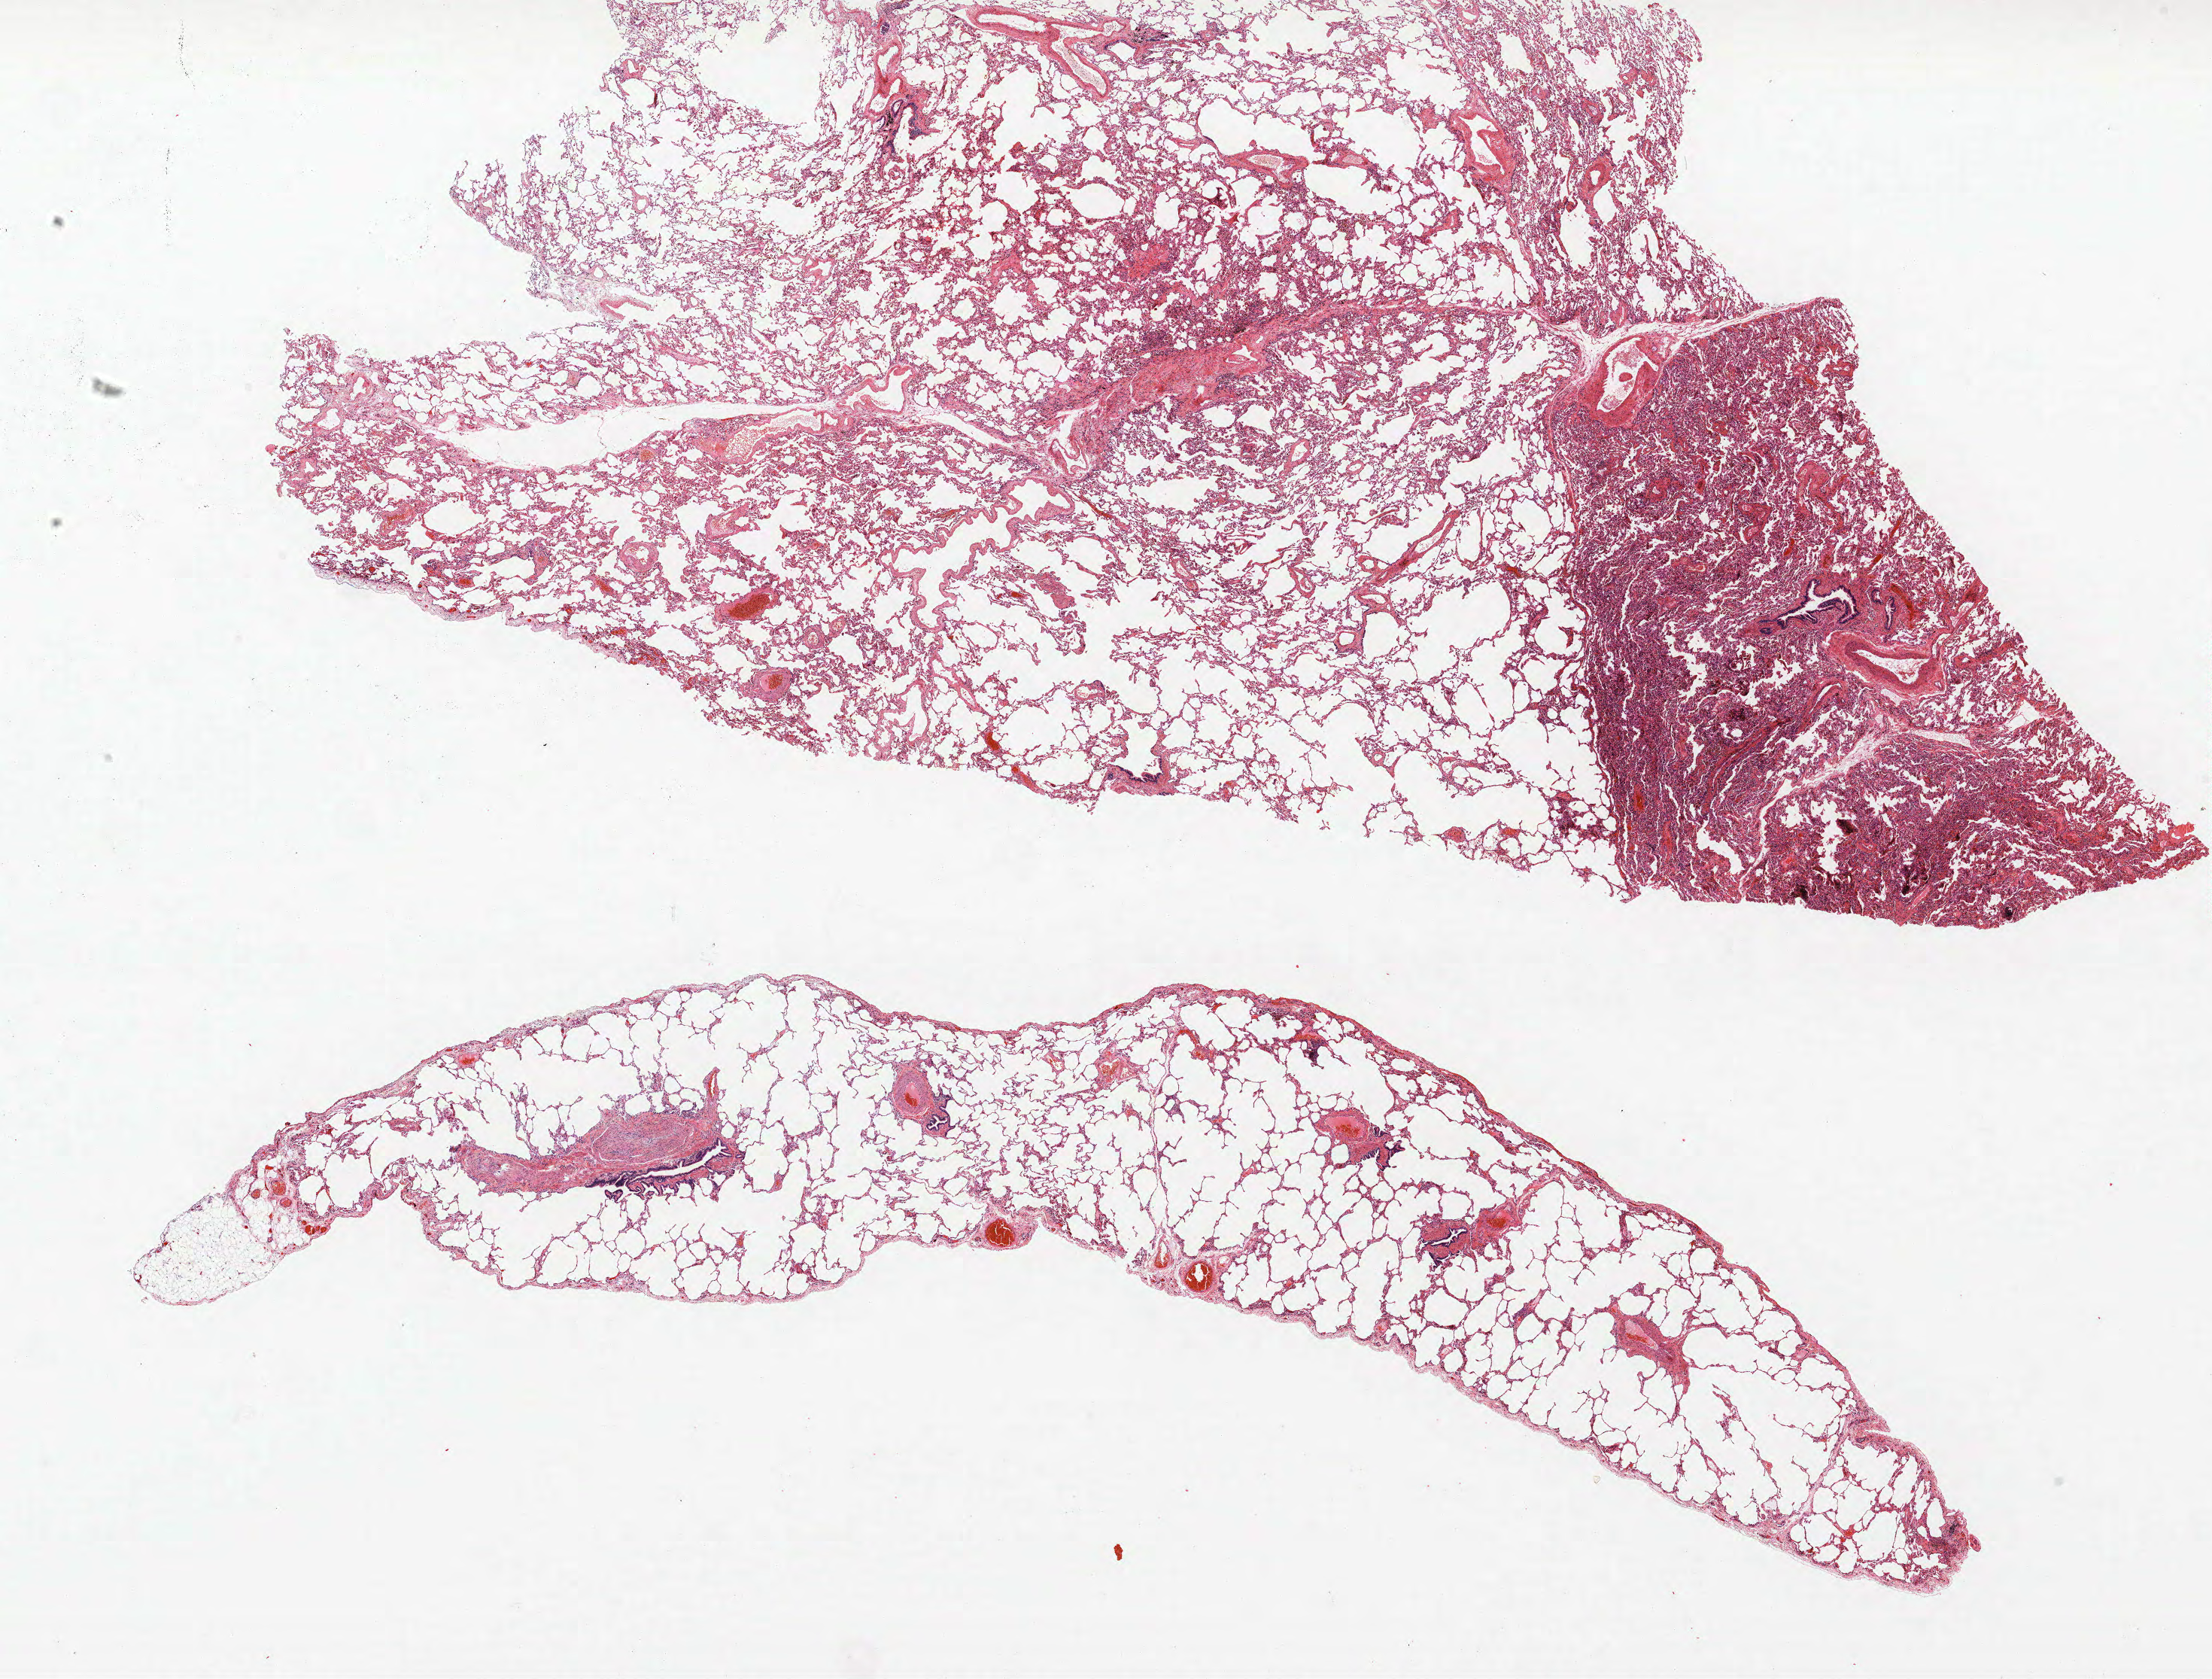
Whole-slide histology image, H&E, a low-resolution overview of the entire scanned area, about 23.5 x 17.9 mm (from a 40x scan); FFPE section; lung. Male patient, aged 61 at enrolment. Grade: well differentiated (G1).
* primary tumour location (clinical record): right middle lobe
* ICD-O-3 topography: middle lobe of lung (C34.2)
* participant's lung-cancer diagnosis: Bronchiolo-alveolar adenocarcinoma, NOS
* tumour size (pathology): 15 mm
* stage (AJCC 6th edition): IA